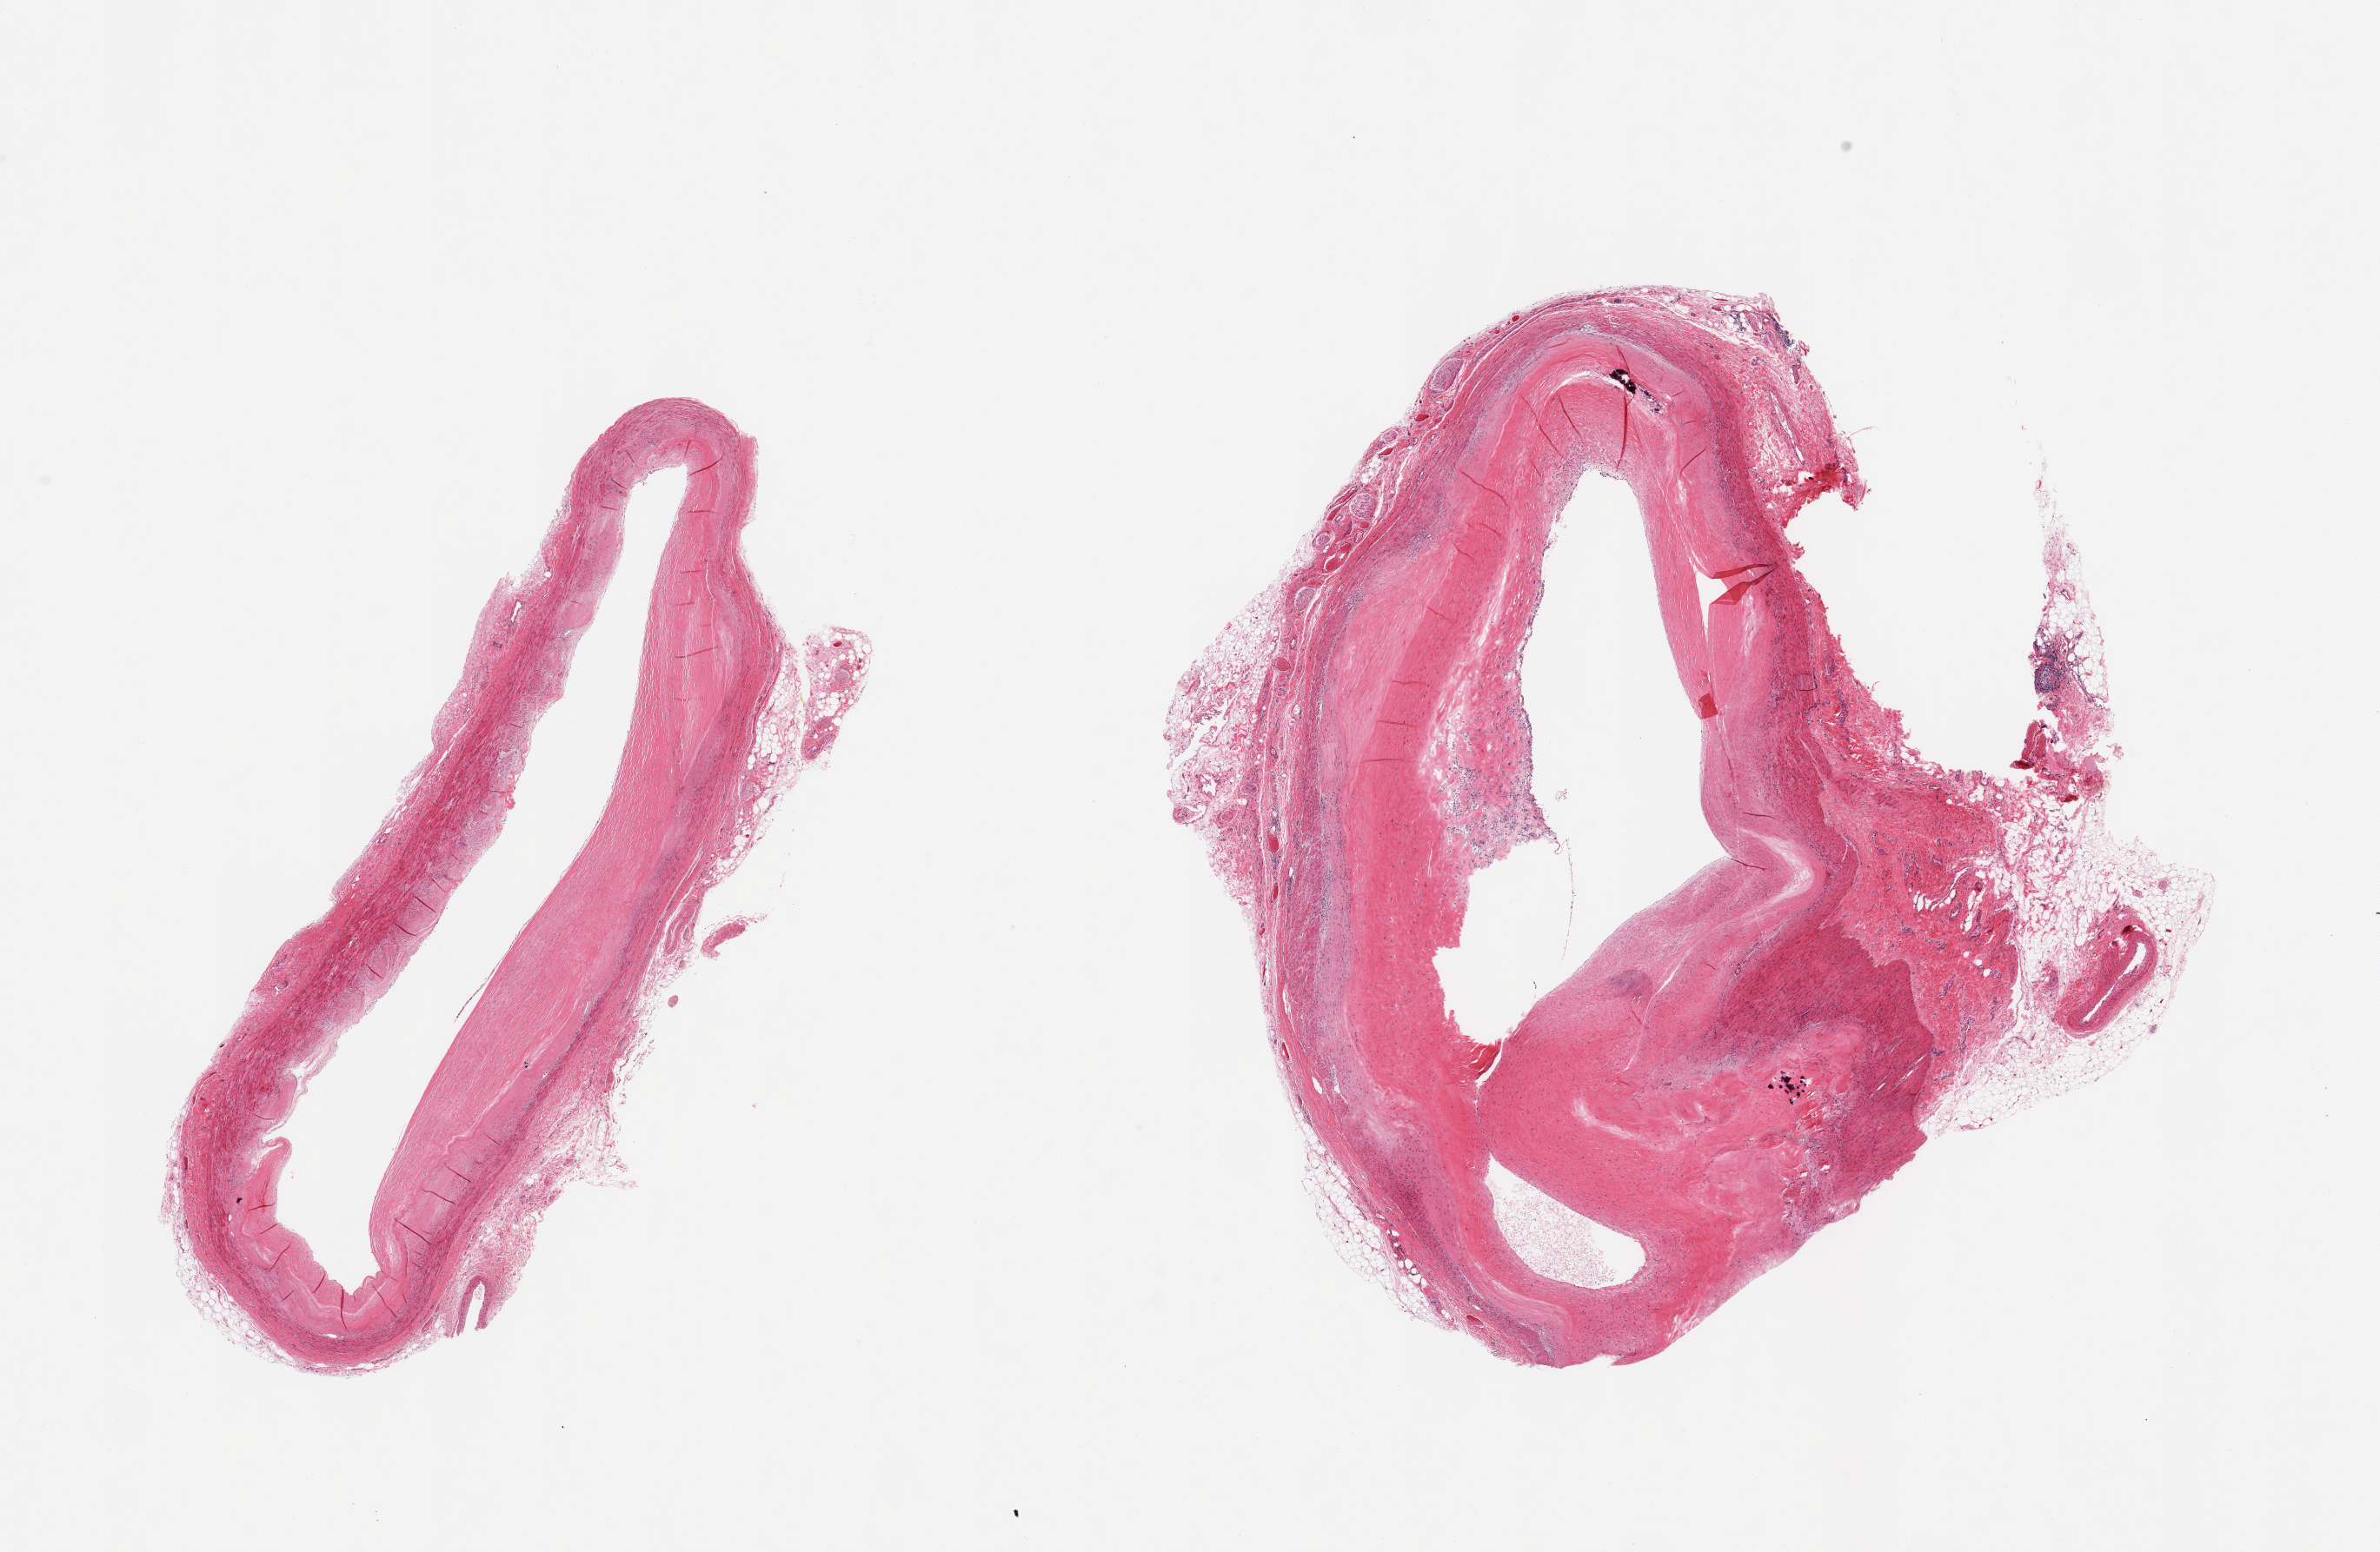
Digitized hematoxylin and eosin (H&E)-stained section — low-resolution overview of the scanned area, about 21.7 x 14.1 mm (from a 20x scan), PAXgene-fixed paraffin-embedded (PFPE) section, target tissue: coronary artery, donor tissue sample. Male donor.
• reviewer comment on this tissue sample: 2 pieces; large eccentric atheromatous and fibrous plaques with small foci of calcium; 10% external fat